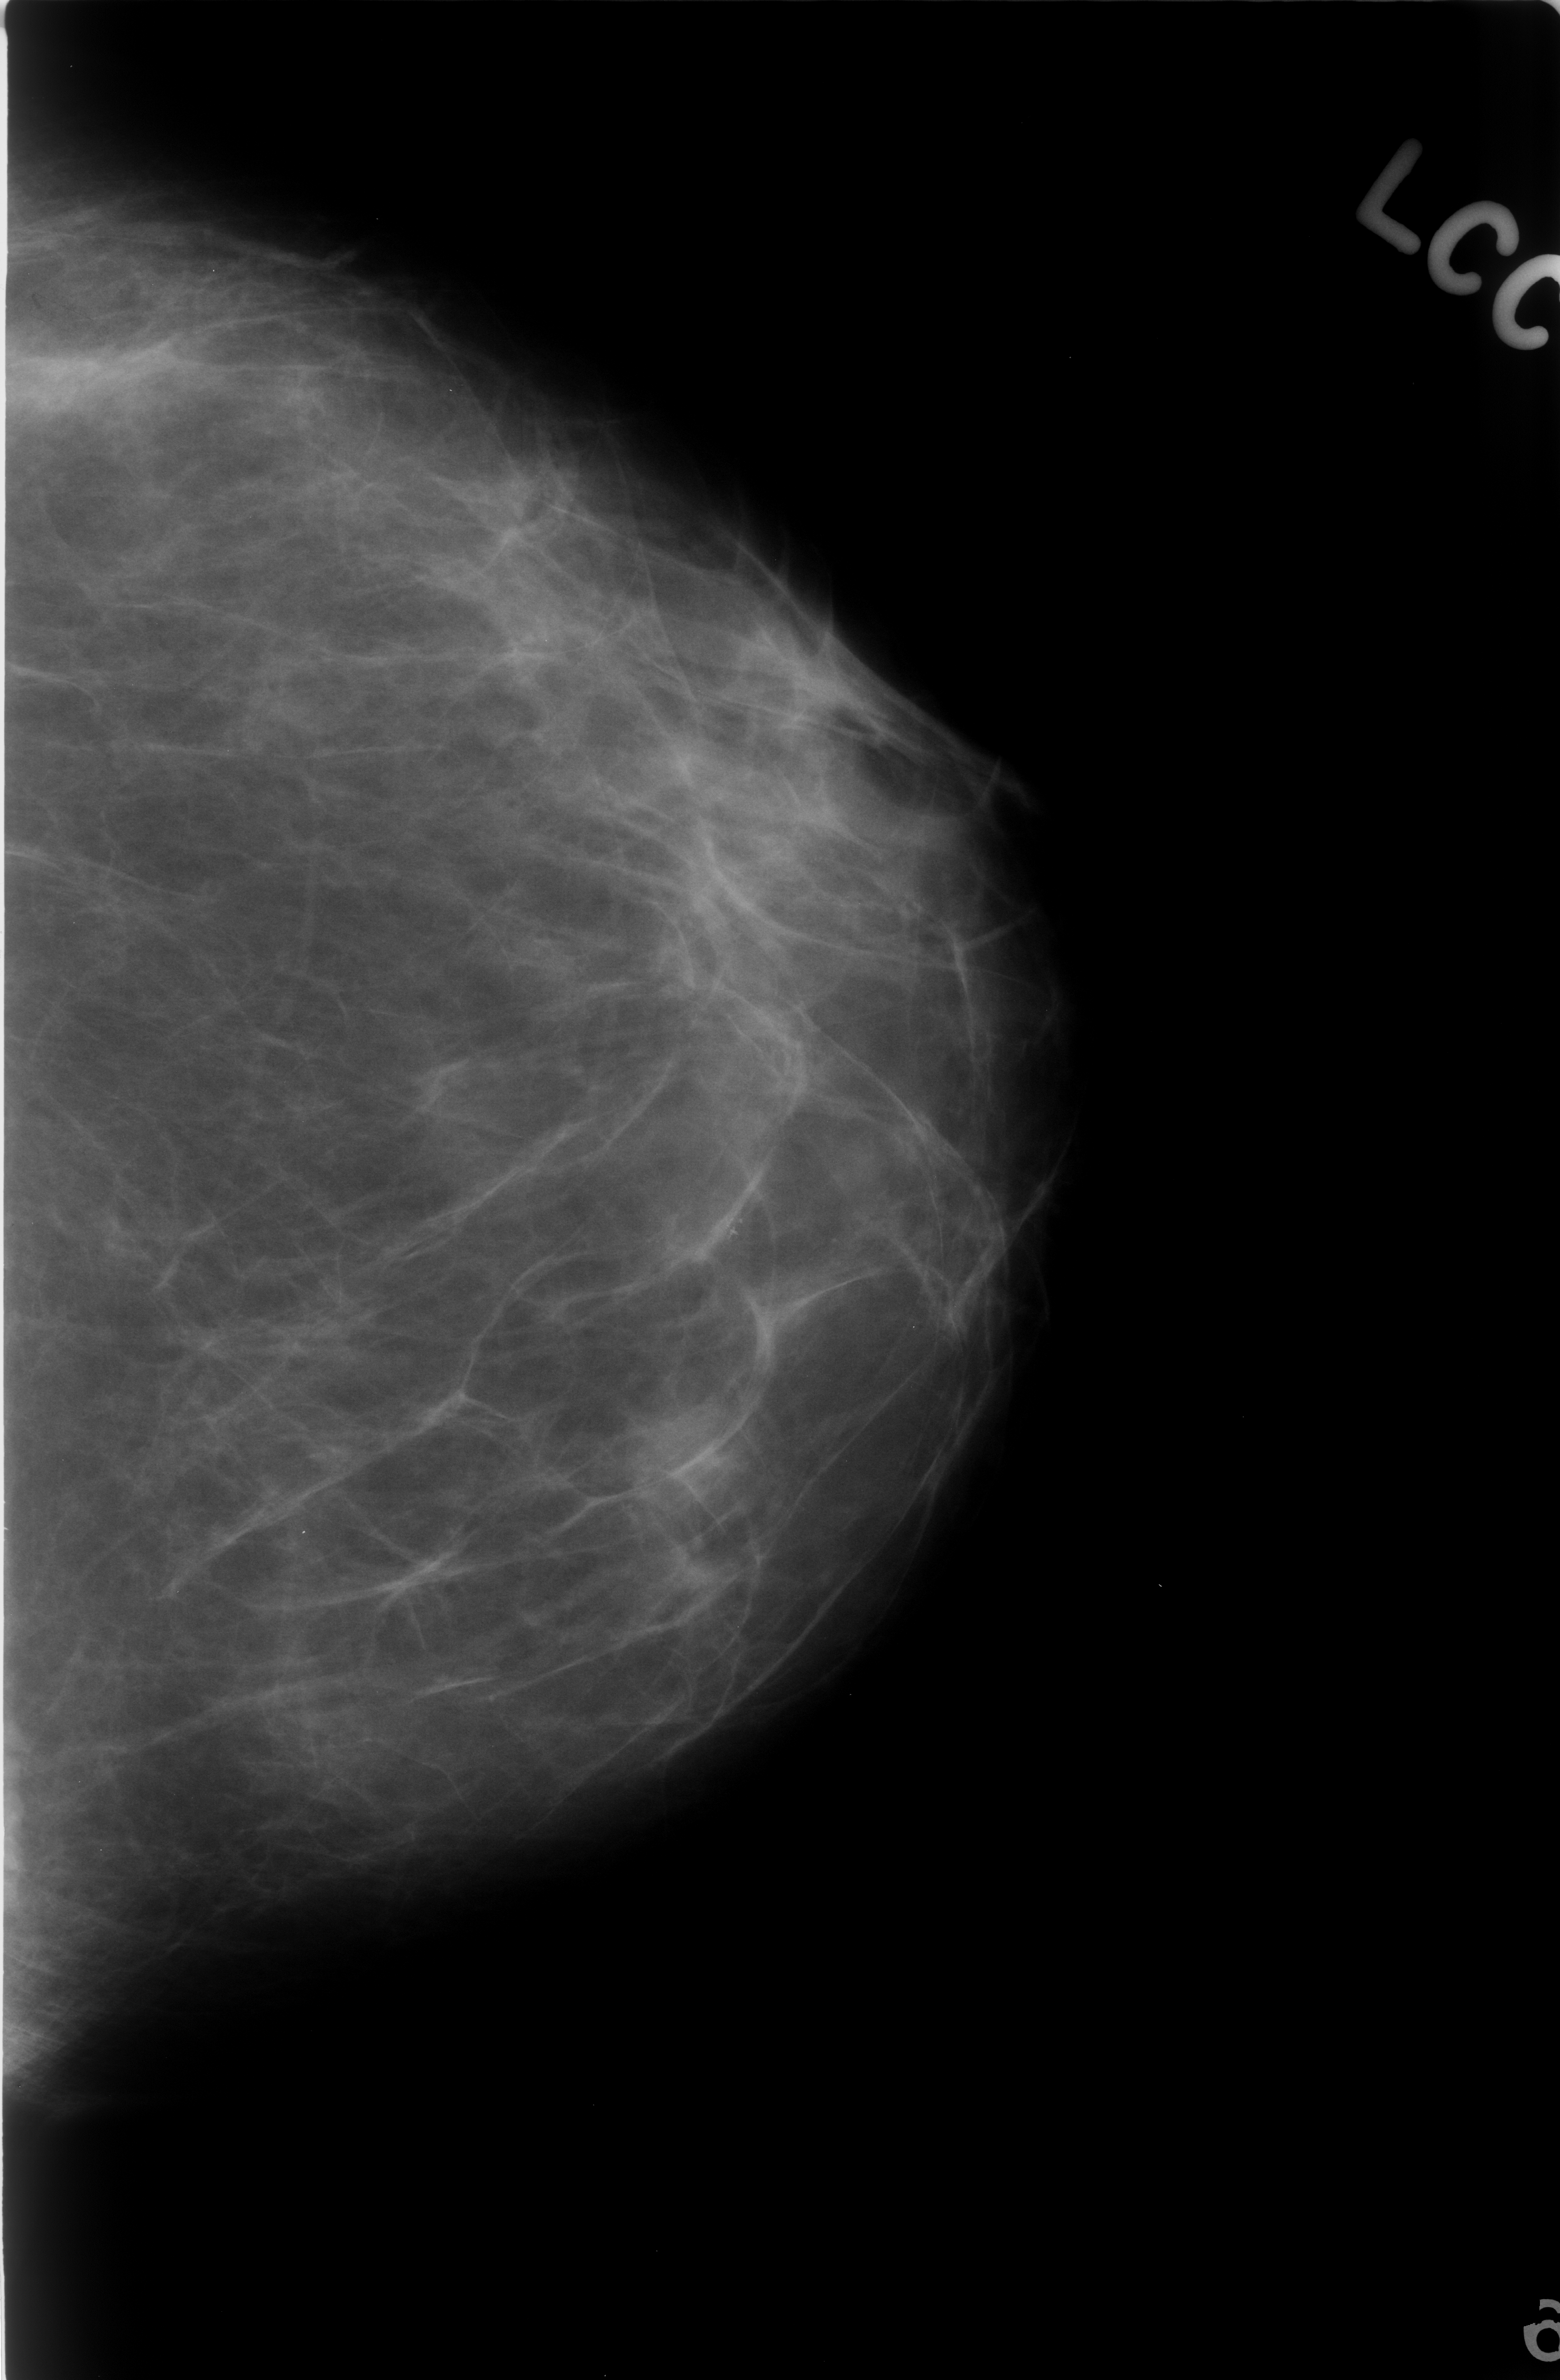
Mammogram (digitized film); left breast; CC view; 1560 × 2380 image matrix.
Marked abnormalities (boxes around the expert regions of interest):
- calcifications, morphology pleomorphic, distribution clustered; BI-RADS assessment category 3; subtlety rating 3 on a 1 (subtle) to 5 (obvious) scale; pathology result (as recorded, not read from the image): benign: bounding box (x1, y1, x2, y2) in pixels: (600, 1365, 796, 1544)